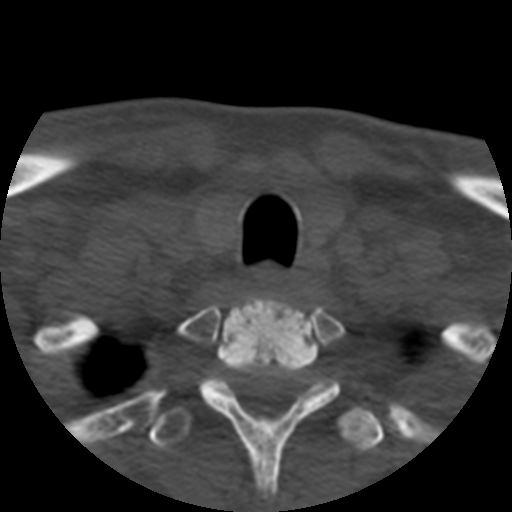
CT including the spine, one axial slice; slice 444 of 508 in the series (ordered by position); reconstruction kernel STANDARD; 120 kVp; bone window (W 1800 / L 400 HU); 1.25 mm slice thickness; 512 × 512 image matrix, field of view 160 × 160 mm. Patient age 57 years. From the clinical record (not read from this slice): primary cancer: prostate.
Outlined on this slice (semi-automatic segmentation, software-assisted and operator-edited):
- T1 vertebra: bounding box <166,297,340,492> (left, top, right, bottom; pixels)
- T2 vertebra: <147,376,387,453>